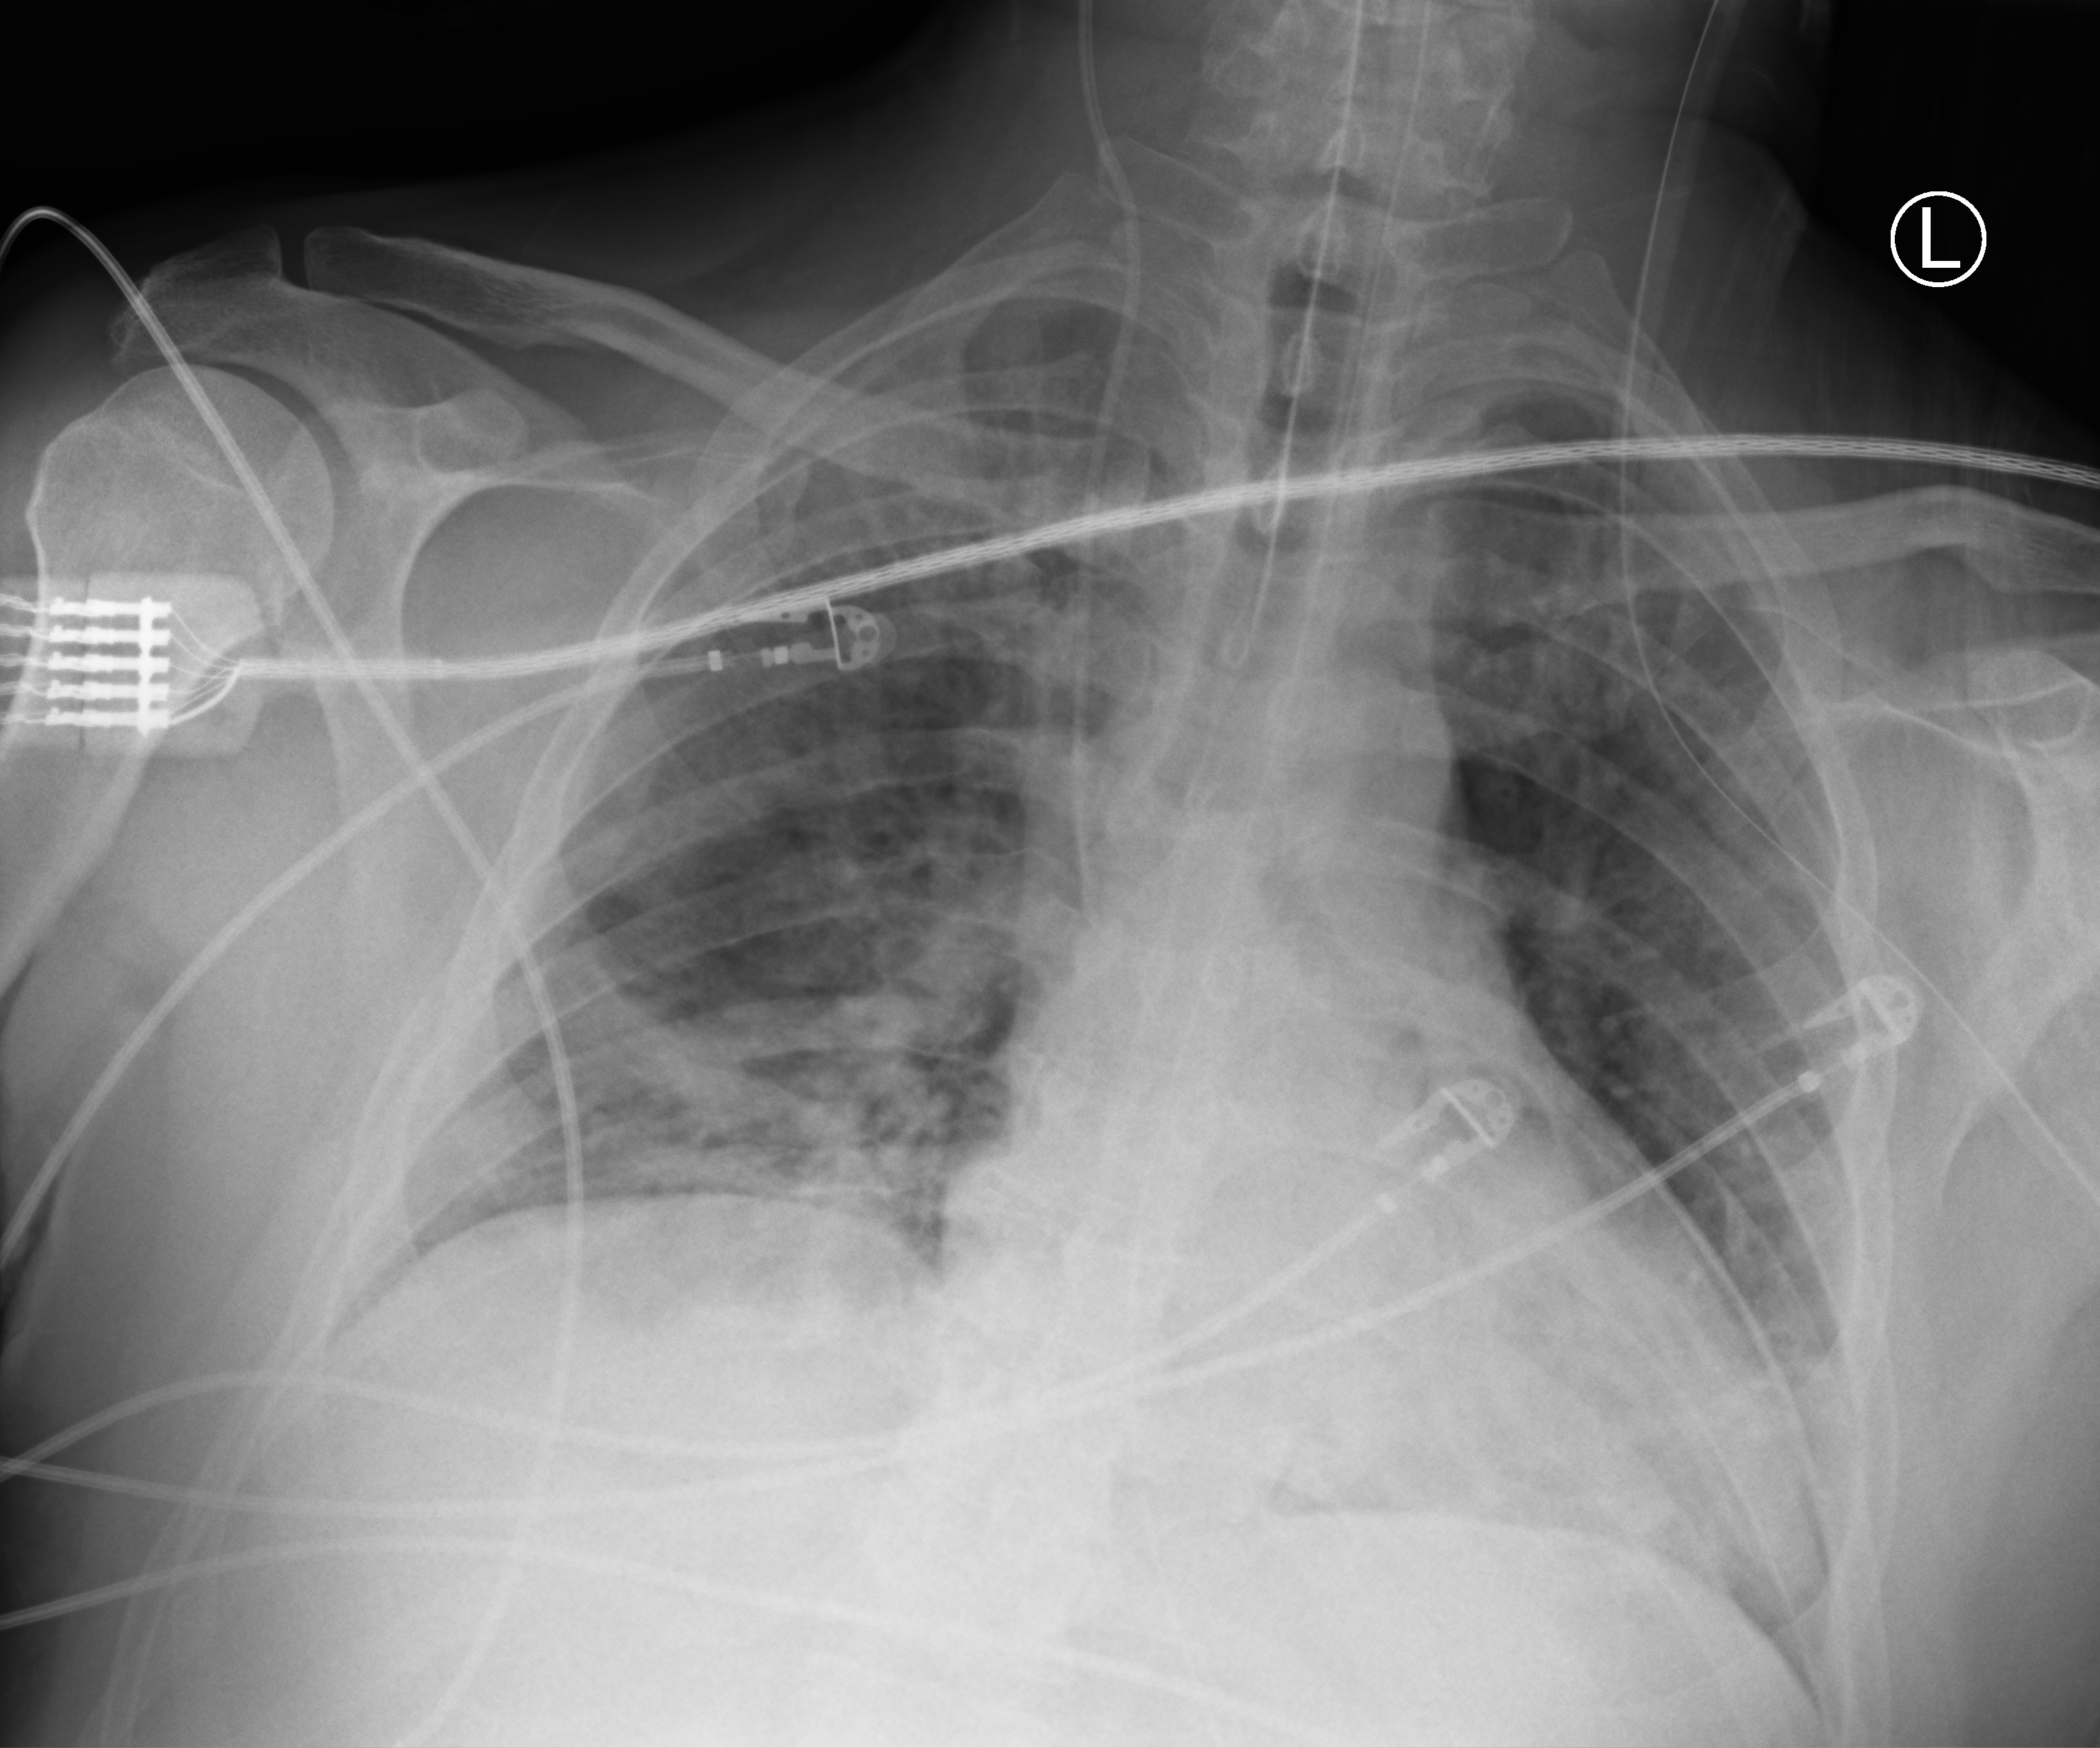
Bedside chest radiograph (computed radiography). Male patient hospitalised with COVID-19, age 18–59 years.
Hospital-stay facts (about this admission, not read from this image; timing relative to this image not recorded): length of hospital stay: 32 days; mechanically ventilated during this hospital stay: yes.